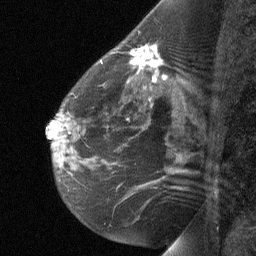
Breast MRI (dynamic contrast-enhanced), one sagittal slice. Position 38 of 64 along the scan axis. Dynamic contrast-enhanced study with each time point stored as its own series, time point 2 of 3 at this slice position (early post-contrast, ordered by acquisition time). 1.5 T. TE 4.8 ms, TR 27 ms. 256 × 256 image matrix, field of view 180 × 180 mm. Patient: female, 51 years. From the clinical record (not read from this slice): setting: breast cancer imaged before/during neoadjuvant chemotherapy; receptor status: HR-positive, HER2-negative.
Annotated regions visible in this slice (semi-automatically segmented with operator editing):
- analysis volume of interest (the breast-tissue region the enhancement analysis was run in; not a lesion): bounding box <81,35,179,103> (left, top, right, bottom; pixels)
- tumour enhancement mask (voxels above the 90 % enhancement threshold inside the analysis volume of interest): <131,45,161,69>